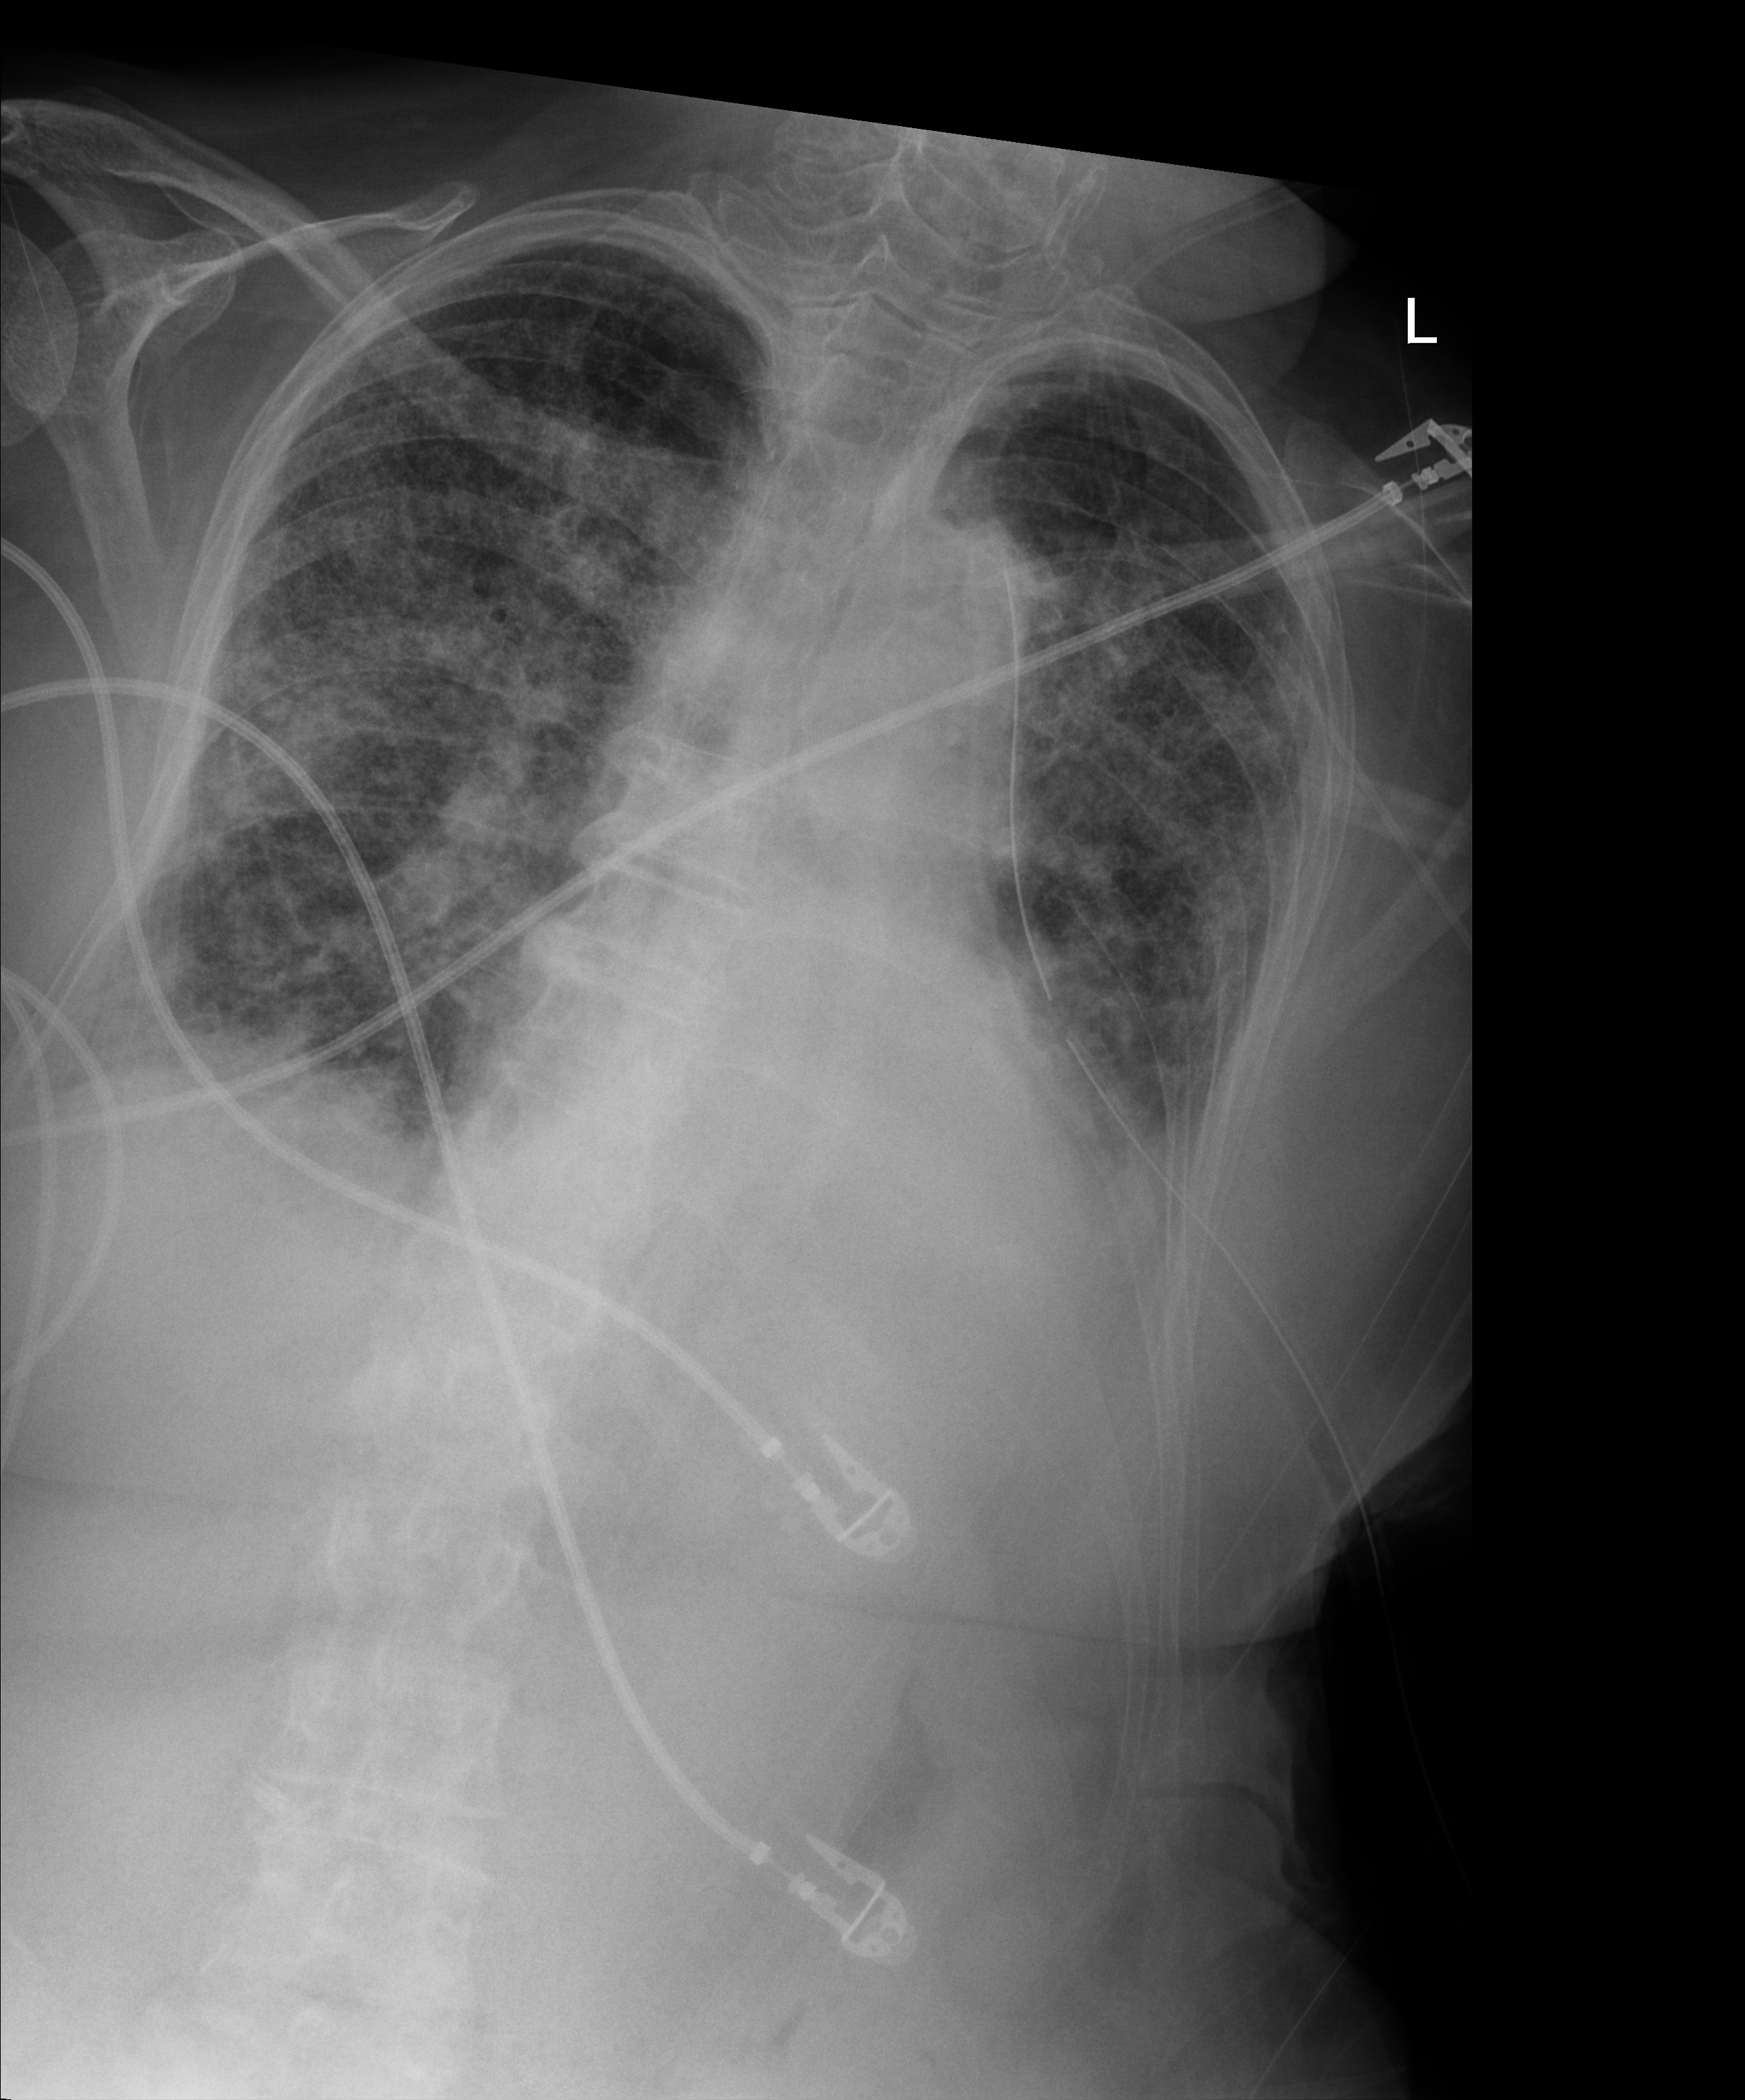
Portable chest radiograph, anteroposterior (AP) projection. Patient hospitalised with COVID-19; female, aged 75–90 years.
Hospital-stay facts (about this admission, not read from this image; timing relative to this image not recorded): length of hospital stay: 70 days; mechanically ventilated during this hospital stay: yes; chronic kidney disease (admission record): no.